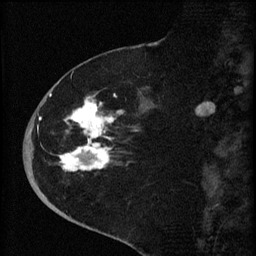
Breast MRI (dynamic contrast-enhanced), one sagittal slice. Dynamic contrast-enhanced series, image 2 of 4 at this slice position (ordered by acquisition). 1.5 T. TE 4.2 ms, TR 8.2 ms. 2 mm slice thickness. 256 × 256 image matrix, field of view 180 × 180 mm. Female patient, age 71 years.
Outlined on this slice (semi-automatically segmented with operator editing):
- analysis volume of interest (the breast-tissue region the enhancement analysis was run in; not a lesion): box from (x=35, y=75) to (x=153, y=190) px
- tumour enhancement mask (voxels above the 70 % enhancement threshold inside the analysis volume of interest): (x=50, y=93)–(x=123, y=172)